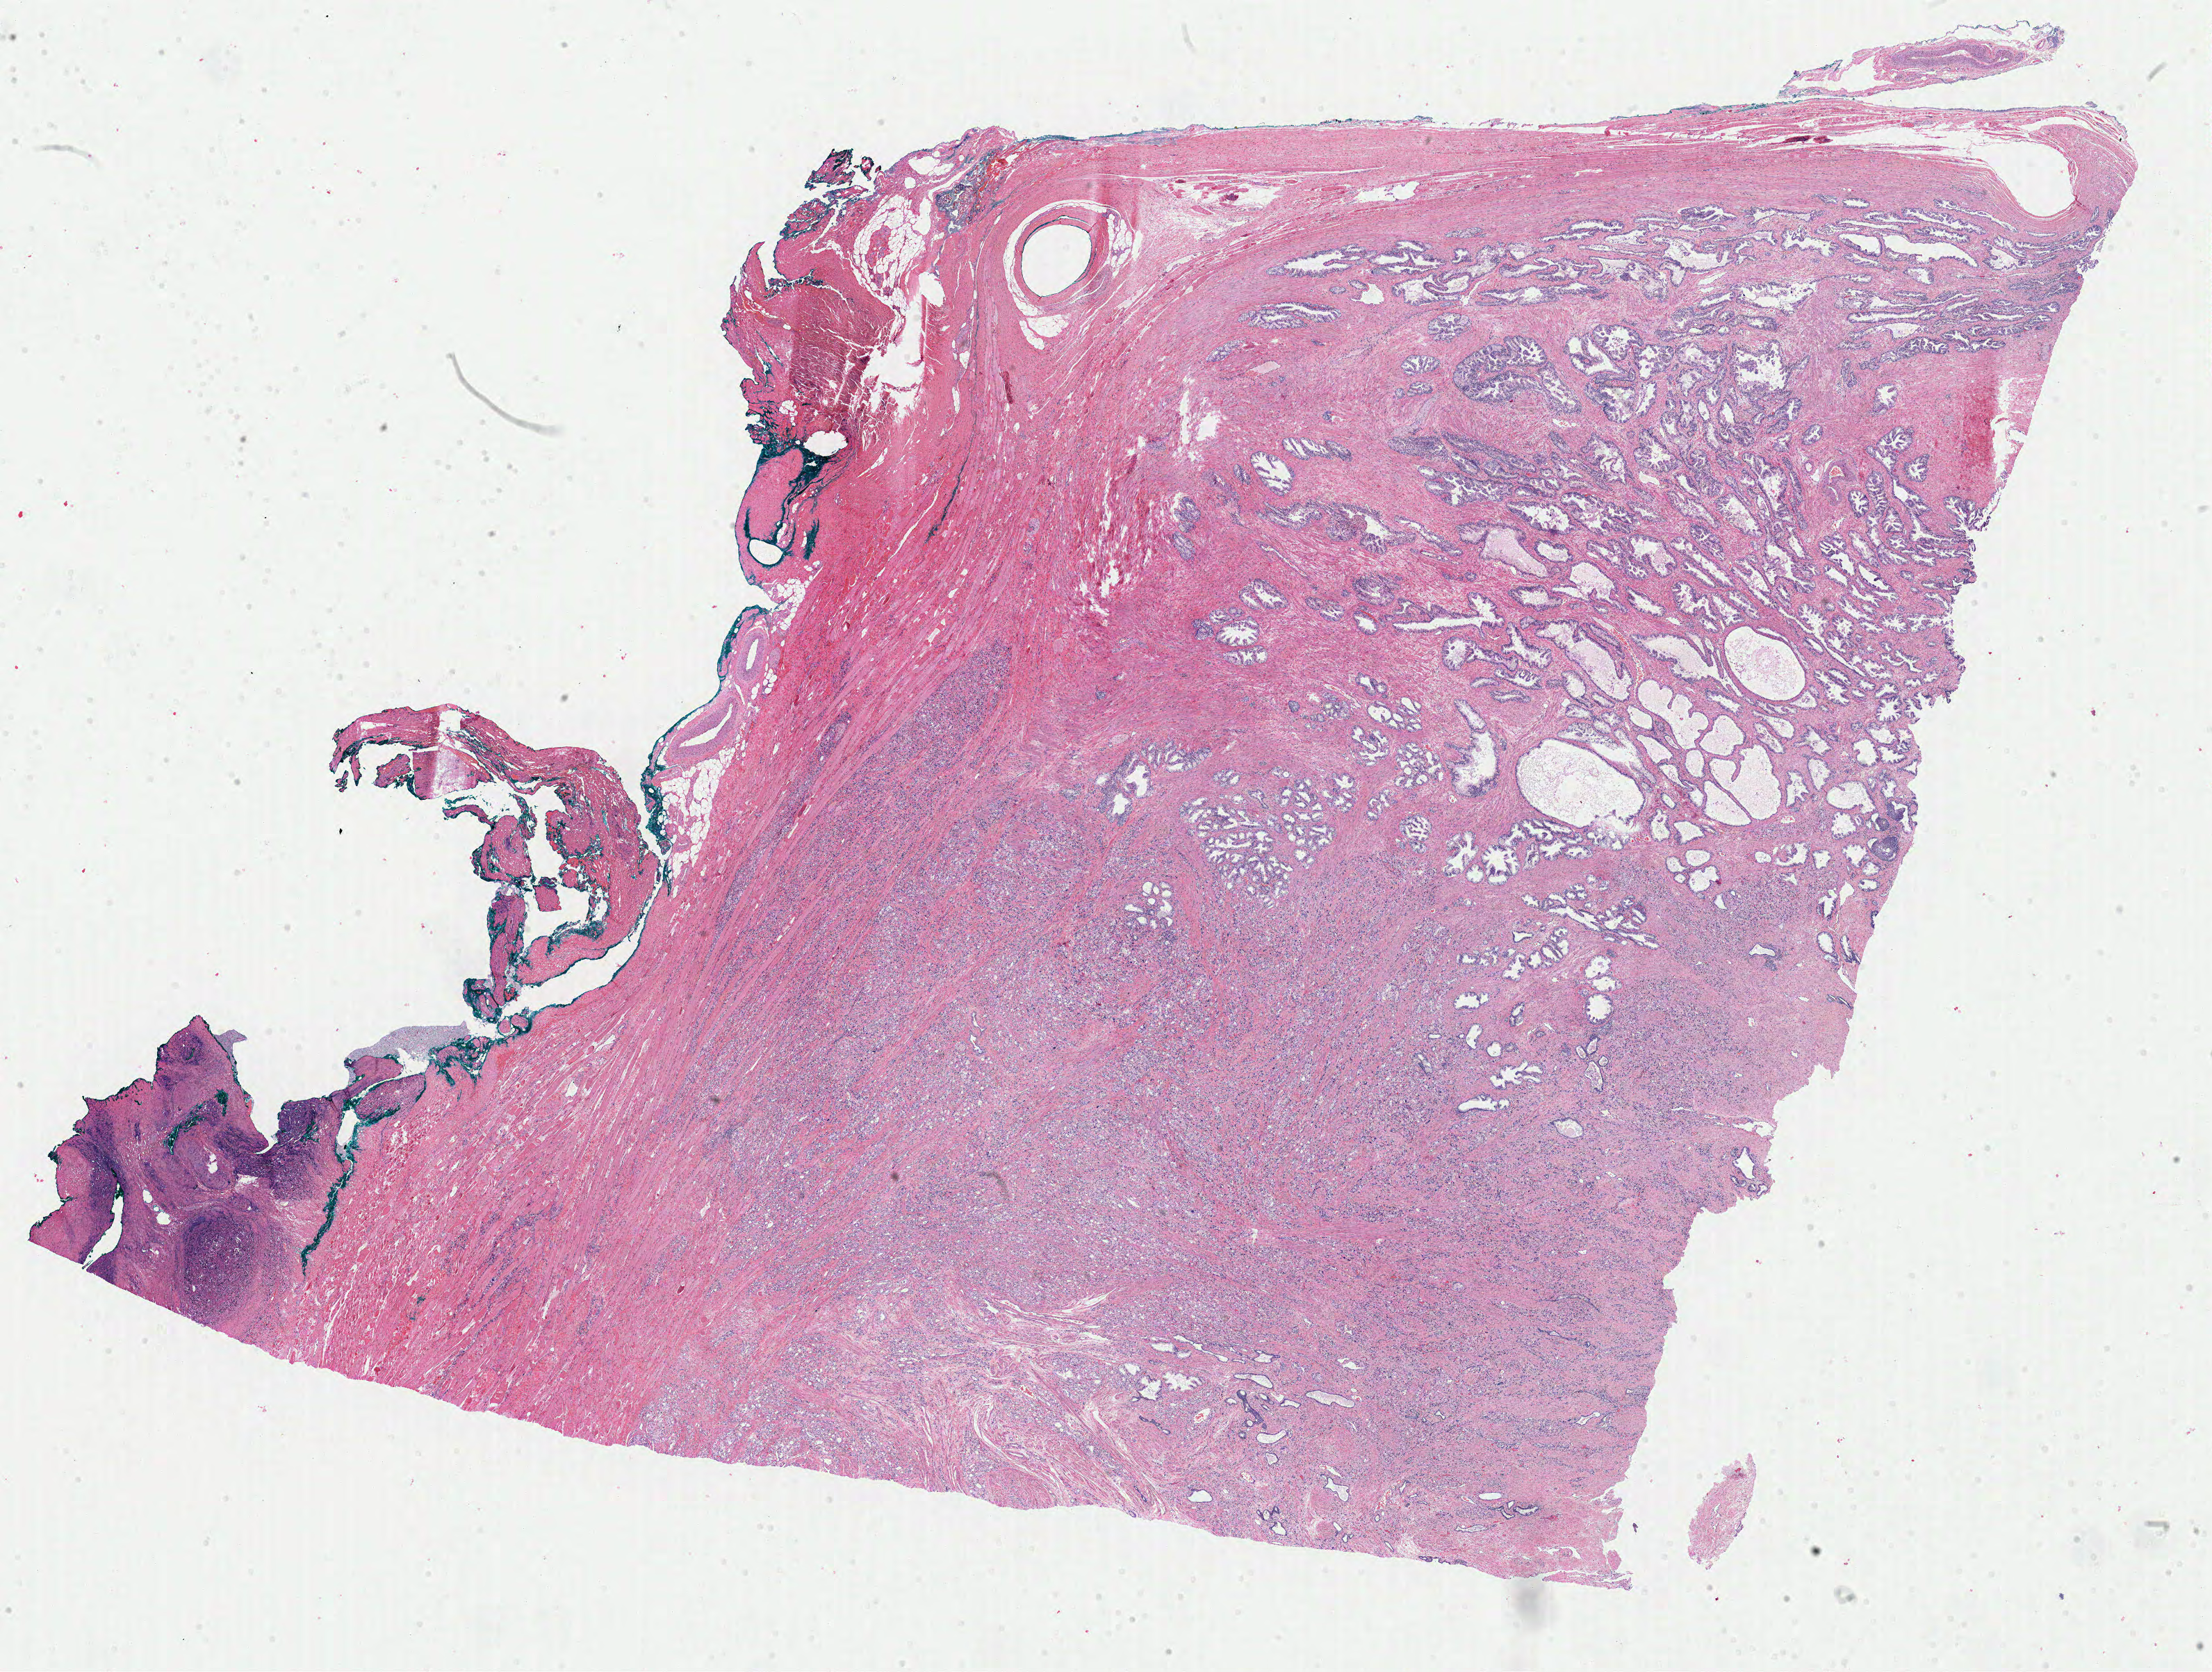
H&E-stained whole-slide image, low-resolution overview of the scanned area, about 25.1 x 19.0 mm (acquisition: 40x scan), FFPE section, primary tumour sample from the prostate. Patient: male, age at initial diagnosis 46 years. Gleason score: 9 (5+4).
Laterality: bilateral. Lymph nodes positive (case pathology): 1 of 11 examined. Histologic diagnosis: Adenocarcinoma, NOS (prostate gland).